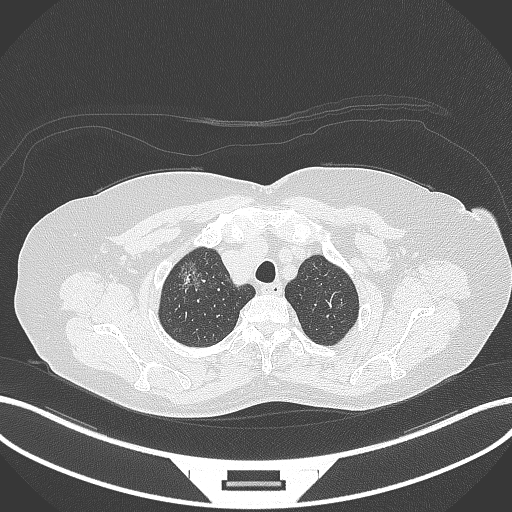
Chest CT, one axial slice; slice 305 of 365 in the series (ordered by position); 120 kVp; lung window (W 1500 / L -600 HU); 1 mm slice thickness; 512 × 512 image matrix, field of view 400 × 400 mm. Female patient, age 62 years. From the clinical record (not read from this slice): clinical TNM (as recorded): T1c N0 M0.
Annotated regions visible in this slice (rectangle marked by the reading radiologist):
- lung tumour (recorded histology: adenocarcinoma): bounding box [x1, y1, x2, y2] px = [176, 253, 218, 298]